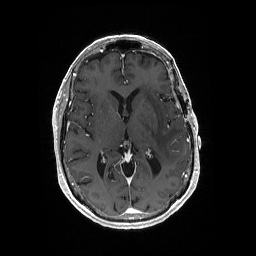
Brain MRI from a brain-tumour surgery series, one axial slice; position 100 of 176 along the scan axis; T1-weighted post-contrast; 1 mm slice thickness; 256 × 256 image matrix, field of view 256 × 256 mm. From the clinical record (not read from this slice): histopathology: Glioblastoma; WHO grade: 4; IDH mutation: no; tumour location: Left Medial Temporal.
Outlined on this slice (outlined manually by an expert reader):
- tumour: bounding box <148,133,151,135> (left, top, right, bottom; pixels)